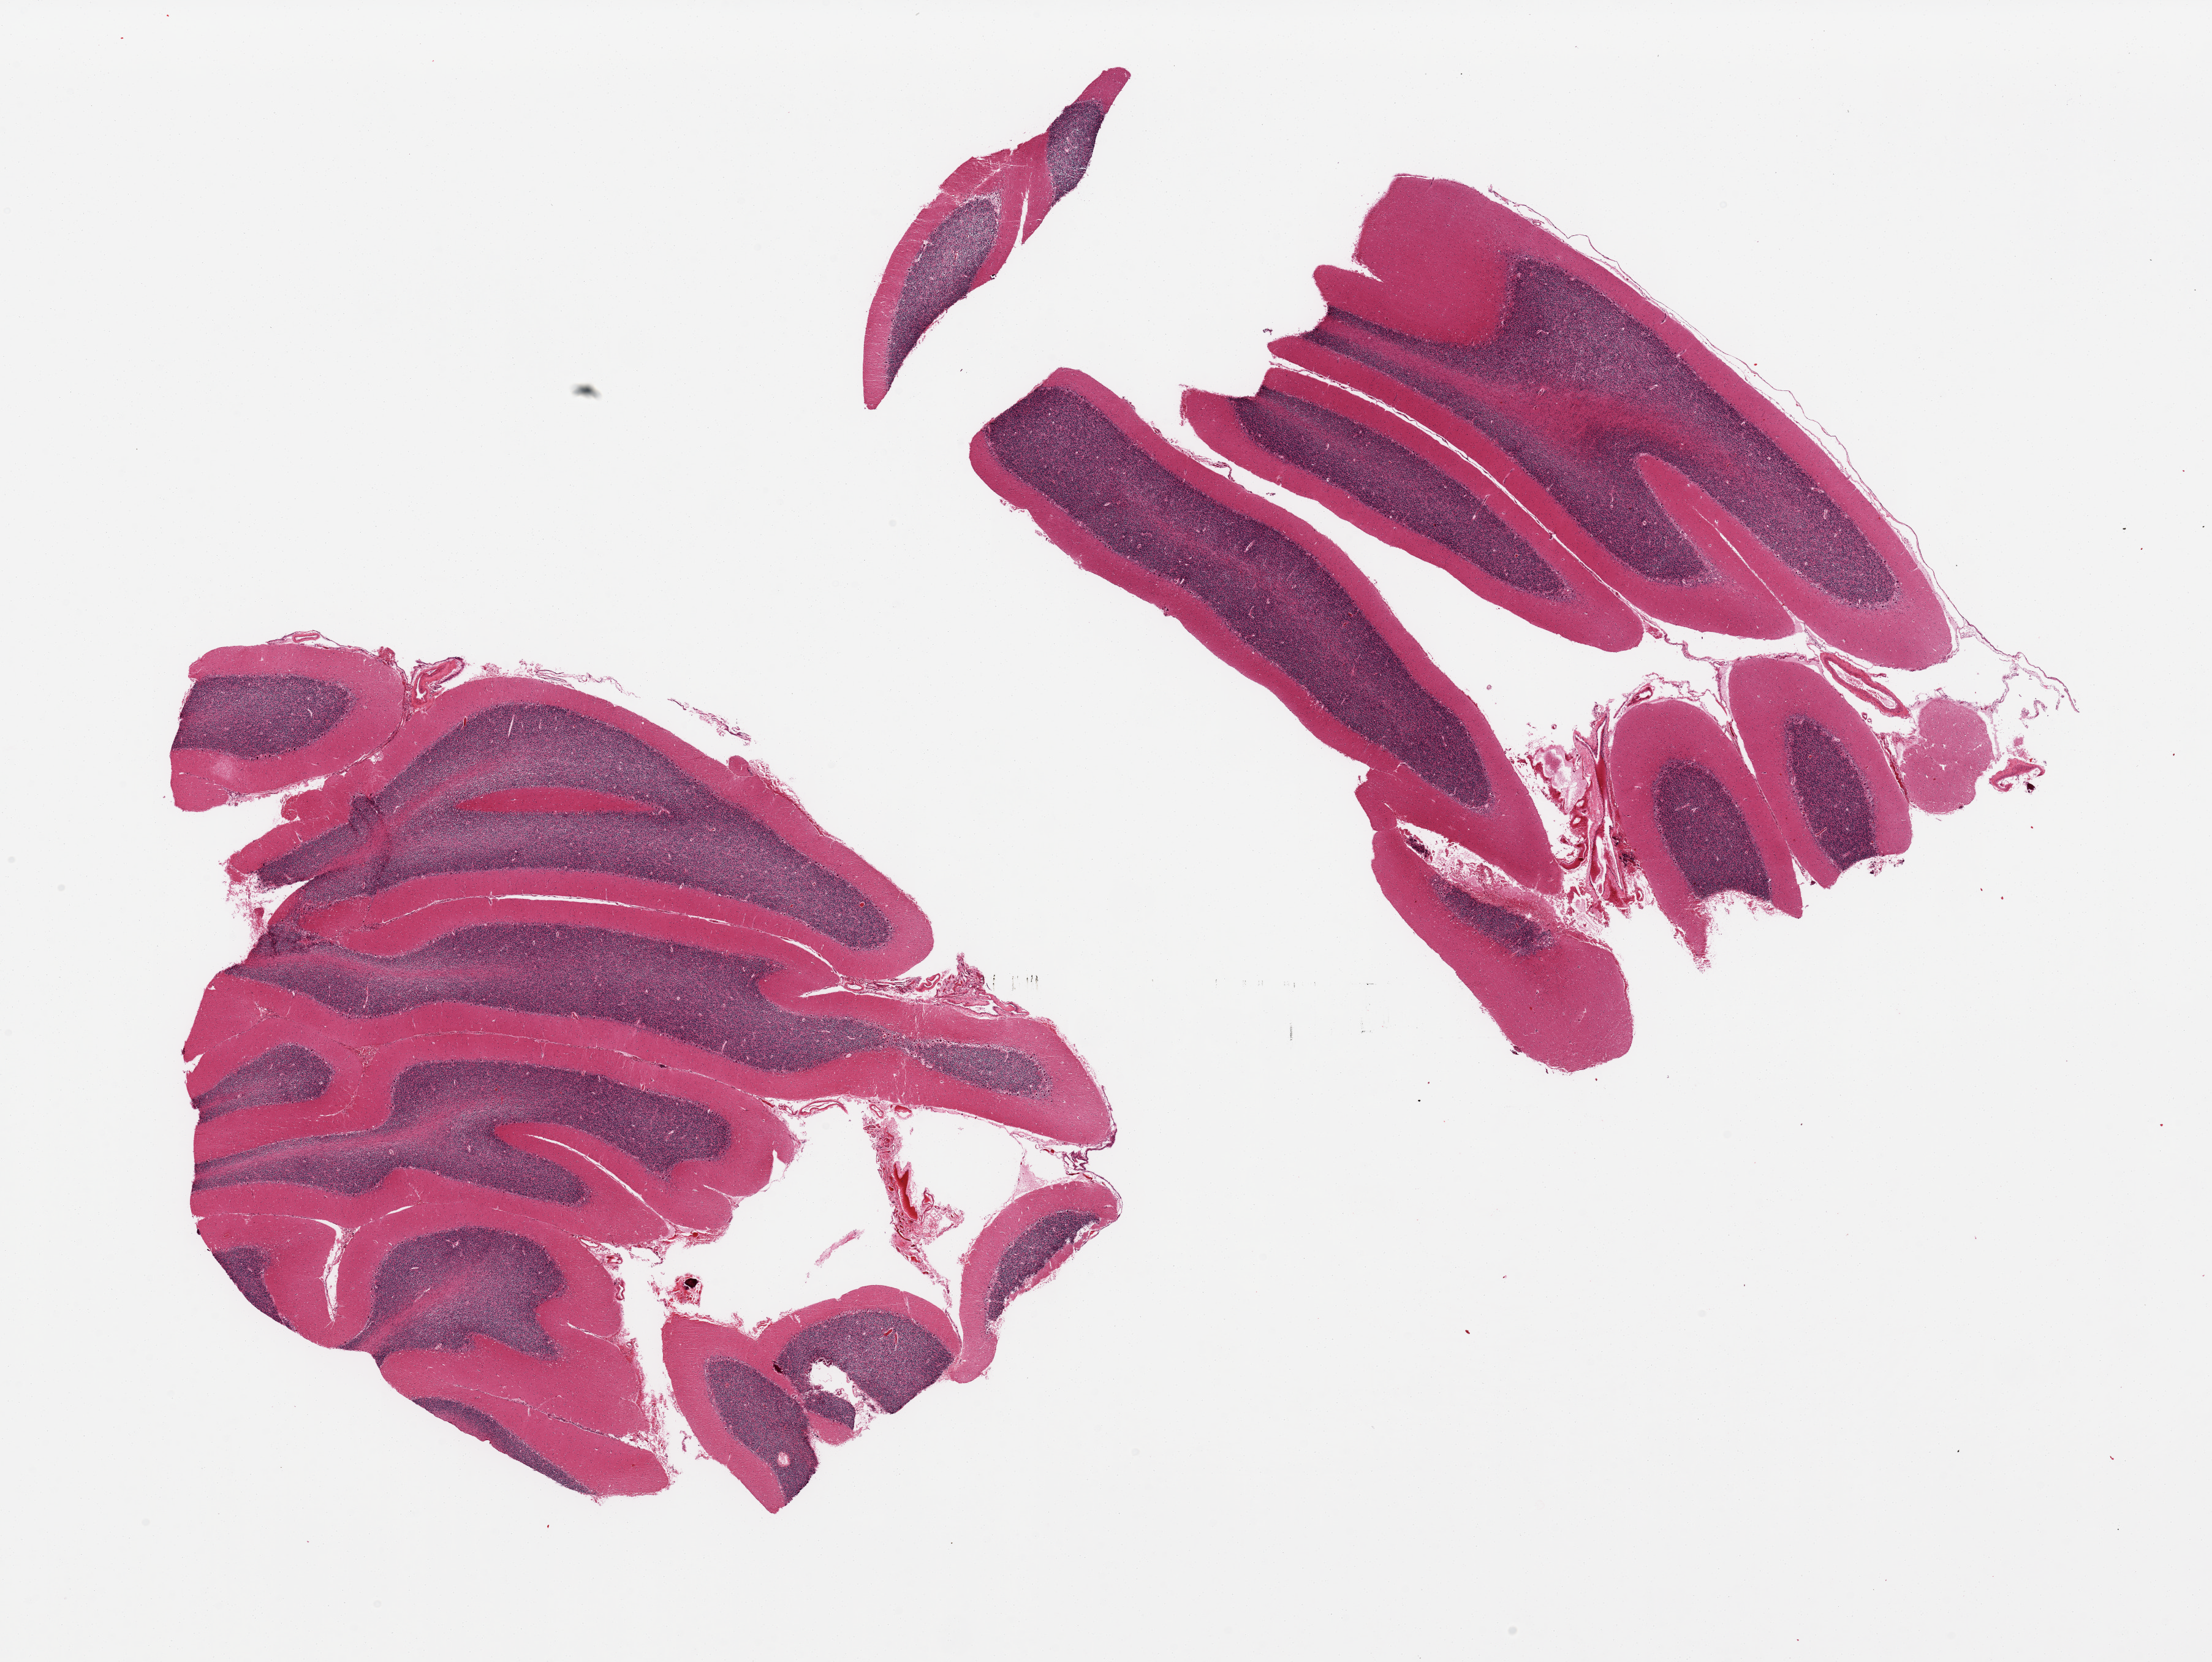
Whole-slide image, haematoxylin and eosin stain, a low-resolution overview of the entire scanned area, about 28.5 x 21.4 mm (from a 20x scan), PAXgene-fixed, paraffin-embedded tissue, sampled site (target tissue): cerebellum, donor tissue sample. Donor: male.
* pathologist's review note for this sample: 3 pieces, Purkinje cells with ? minimal hypoxic change